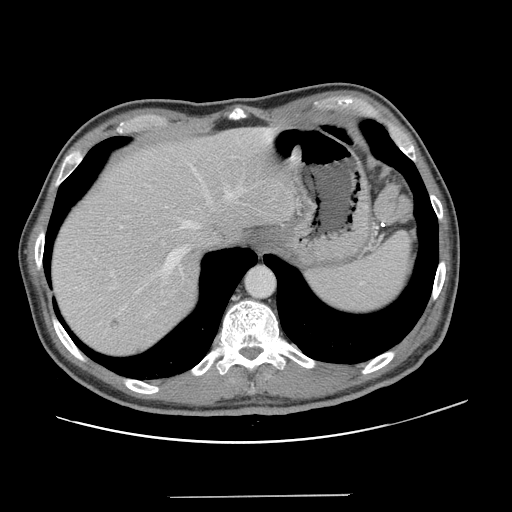
Contrast-enhanced abdominal CT, one axial slice. Slice 107 of 131 in the series (ordered by position). Intravenous contrast given. Soft-tissue window (W 400 / L 40 HU). 2.5 mm slice thickness. 512 × 512 image matrix. Male patient, age 60 years. From the clinical record (not read from this slice): diagnosis: colorectal cancer liver metastases, imaged before liver resection; multiple liver metastases: no; largest metastasis: 2.5 cm.
Outlined on this slice (manually delineated by an expert):
- hepatic veins: box from (x=121, y=164) to (x=243, y=292) px
- liver: (x=51, y=127)–(x=296, y=357)
- planned liver remnant (the part of the liver to remain after resection): (x=51, y=127)–(x=296, y=347)
- portal vein (with intrahepatic branches): (x=111, y=184)–(x=191, y=276)